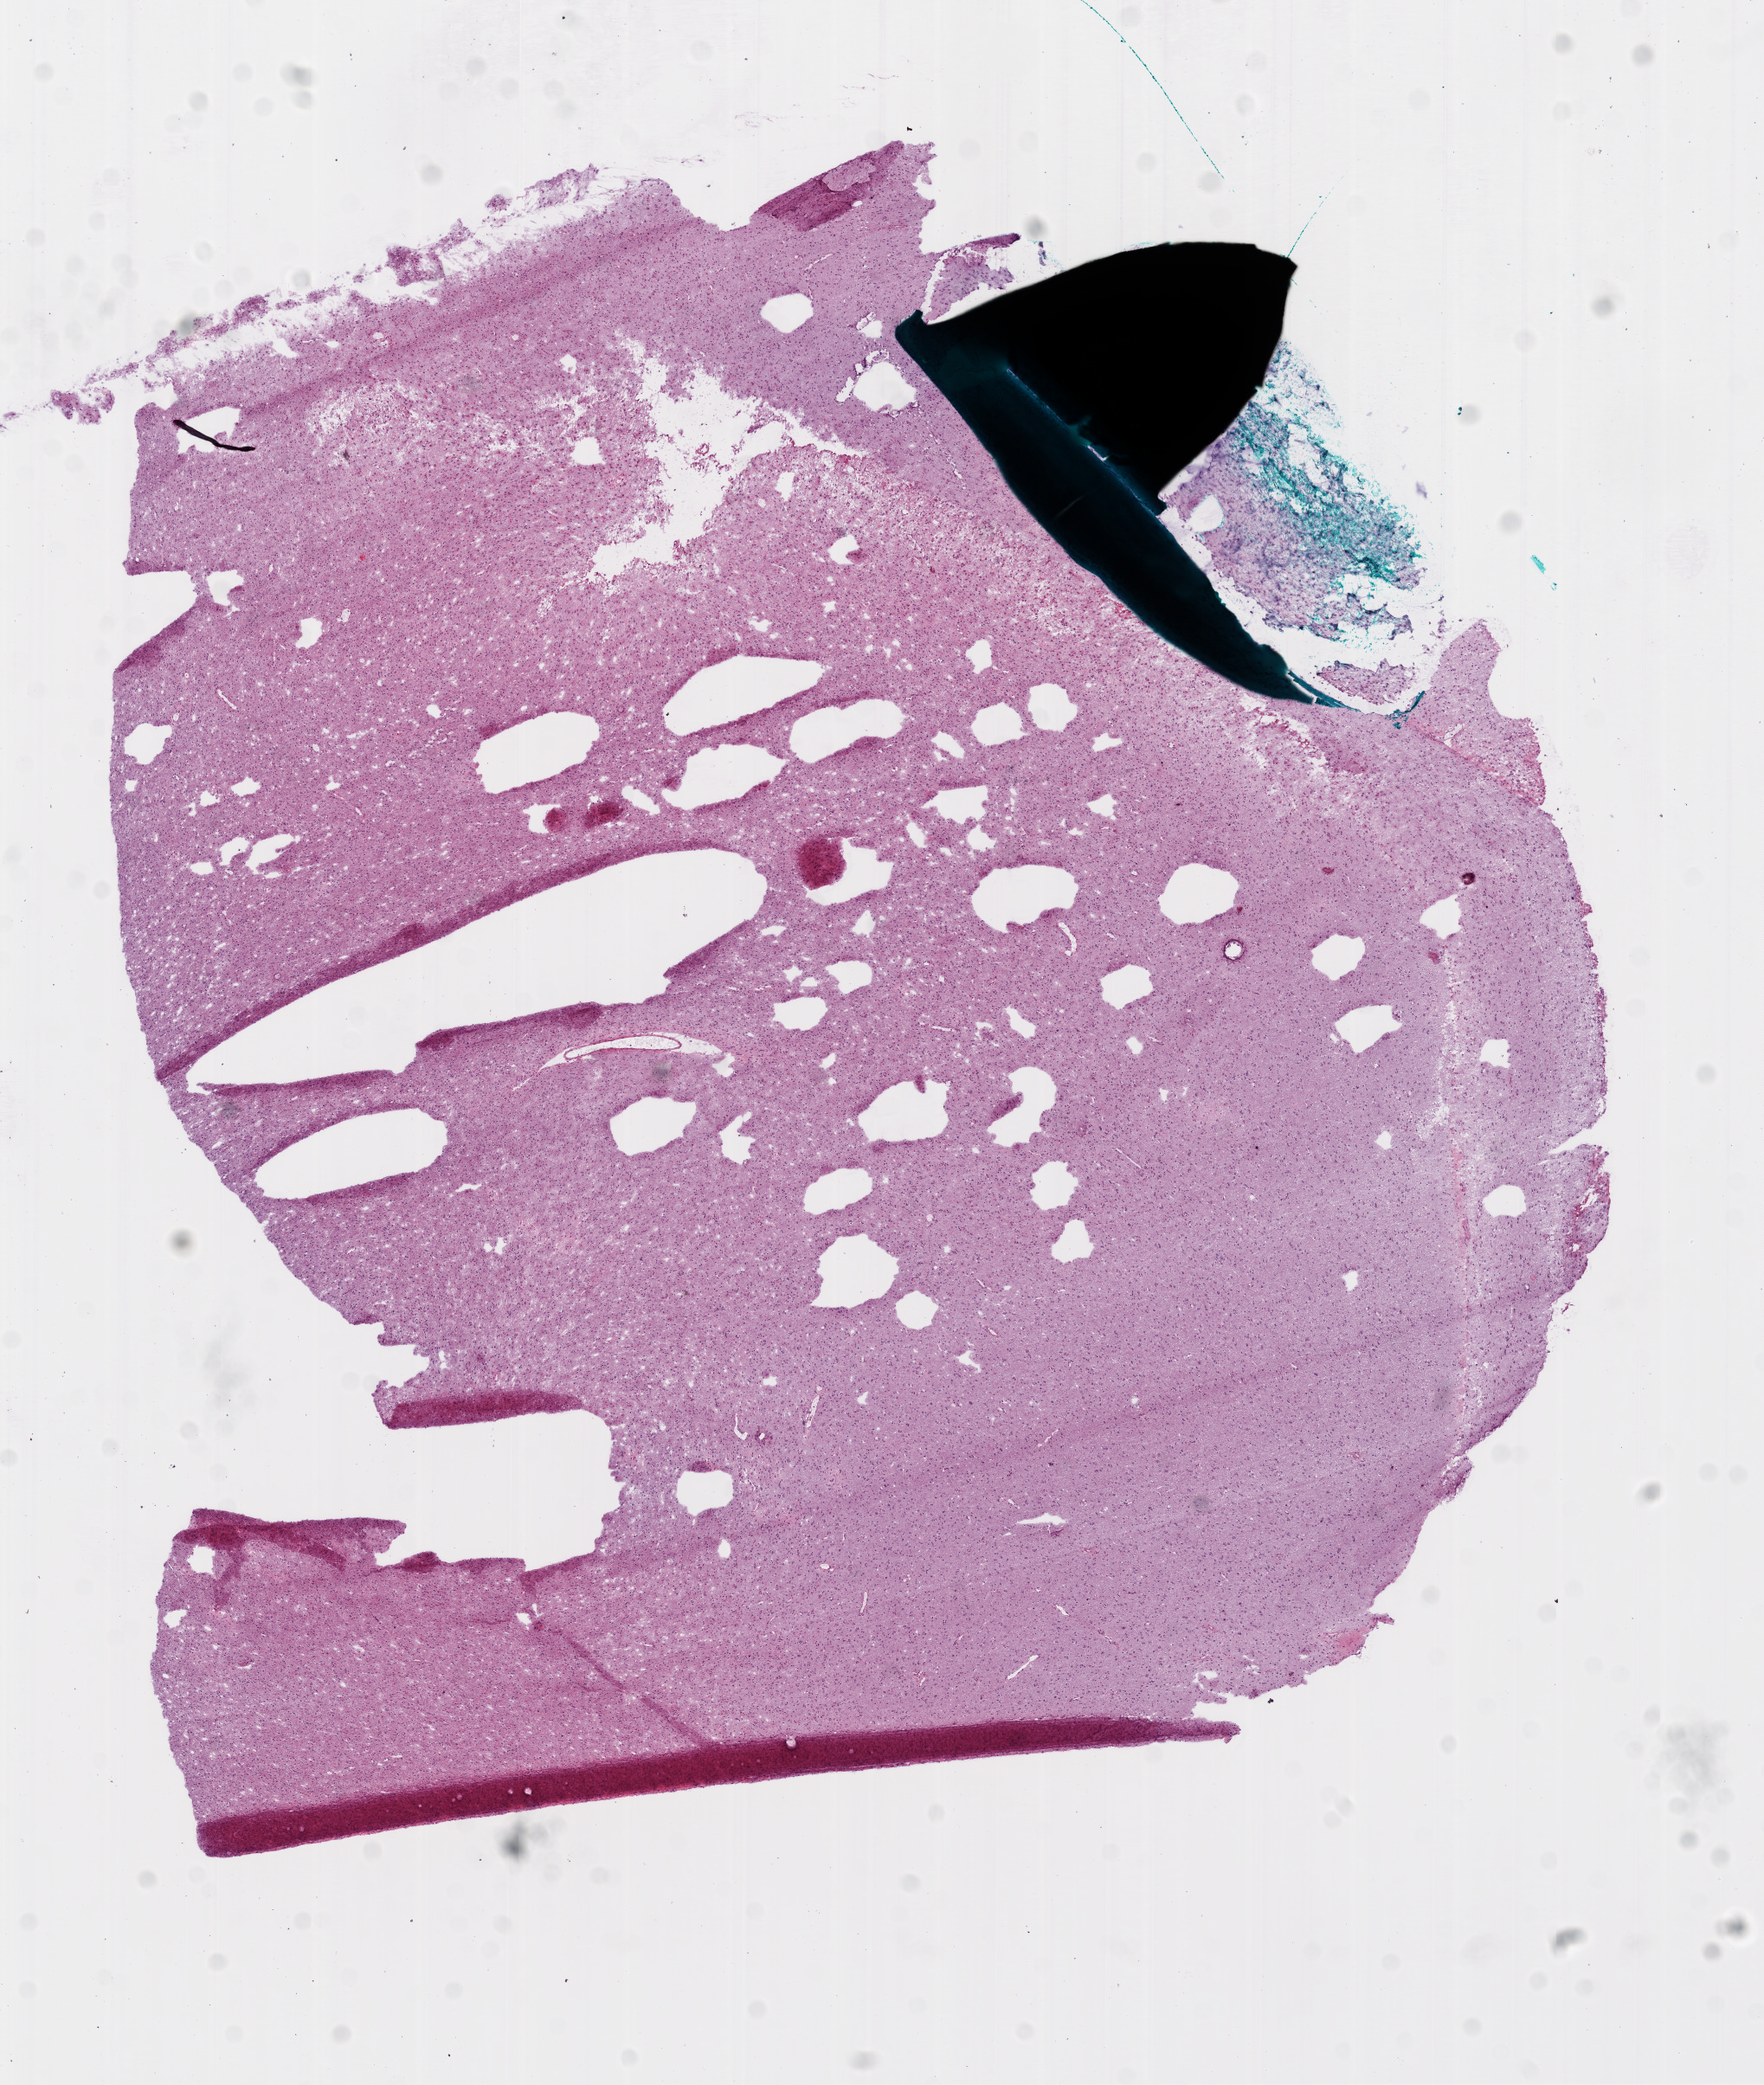
Digitized H&E-stained tissue section (whole slide) — low-resolution overview of the scanned area, about 8.2 x 9.7 mm (slide scanned at 20x). Frozen section from the bottom of the tissue portion. Sample: primary tumour, brain. Patient: male, age at initial diagnosis 50 years. Pathologist review of this section (percent, as recorded): tumour cells 75%, tumour nuclei 85%.
Diagnosis: Glioblastoma.